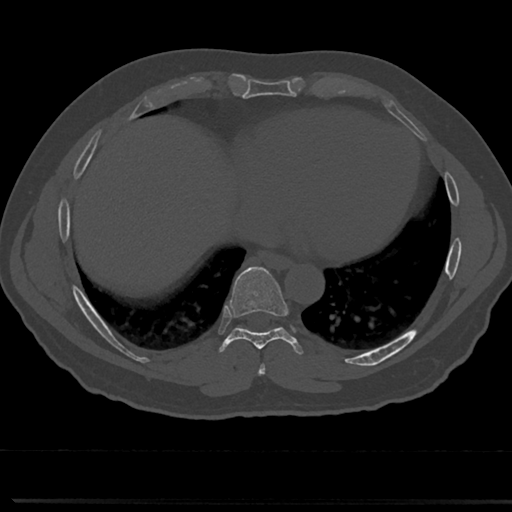
CT including the spine, one axial slice; slice 349 of 817 in the series (ordered by position); reconstruction kernel Br40s/3; 120 kVp; bone window (W 1800 / L 400 HU); 512 × 512 image matrix, field of view 355 × 355 mm. Patient: male, 61 years. Case-level facts recorded for this patient, not image findings: primary cancer: prostate.
Structures marked on this image (semi-automatically segmented with operator editing):
- T7 vertebra: box from (x=254, y=340) to (x=271, y=376) px
- T8 vertebra: (x=219, y=271)–(x=301, y=350)